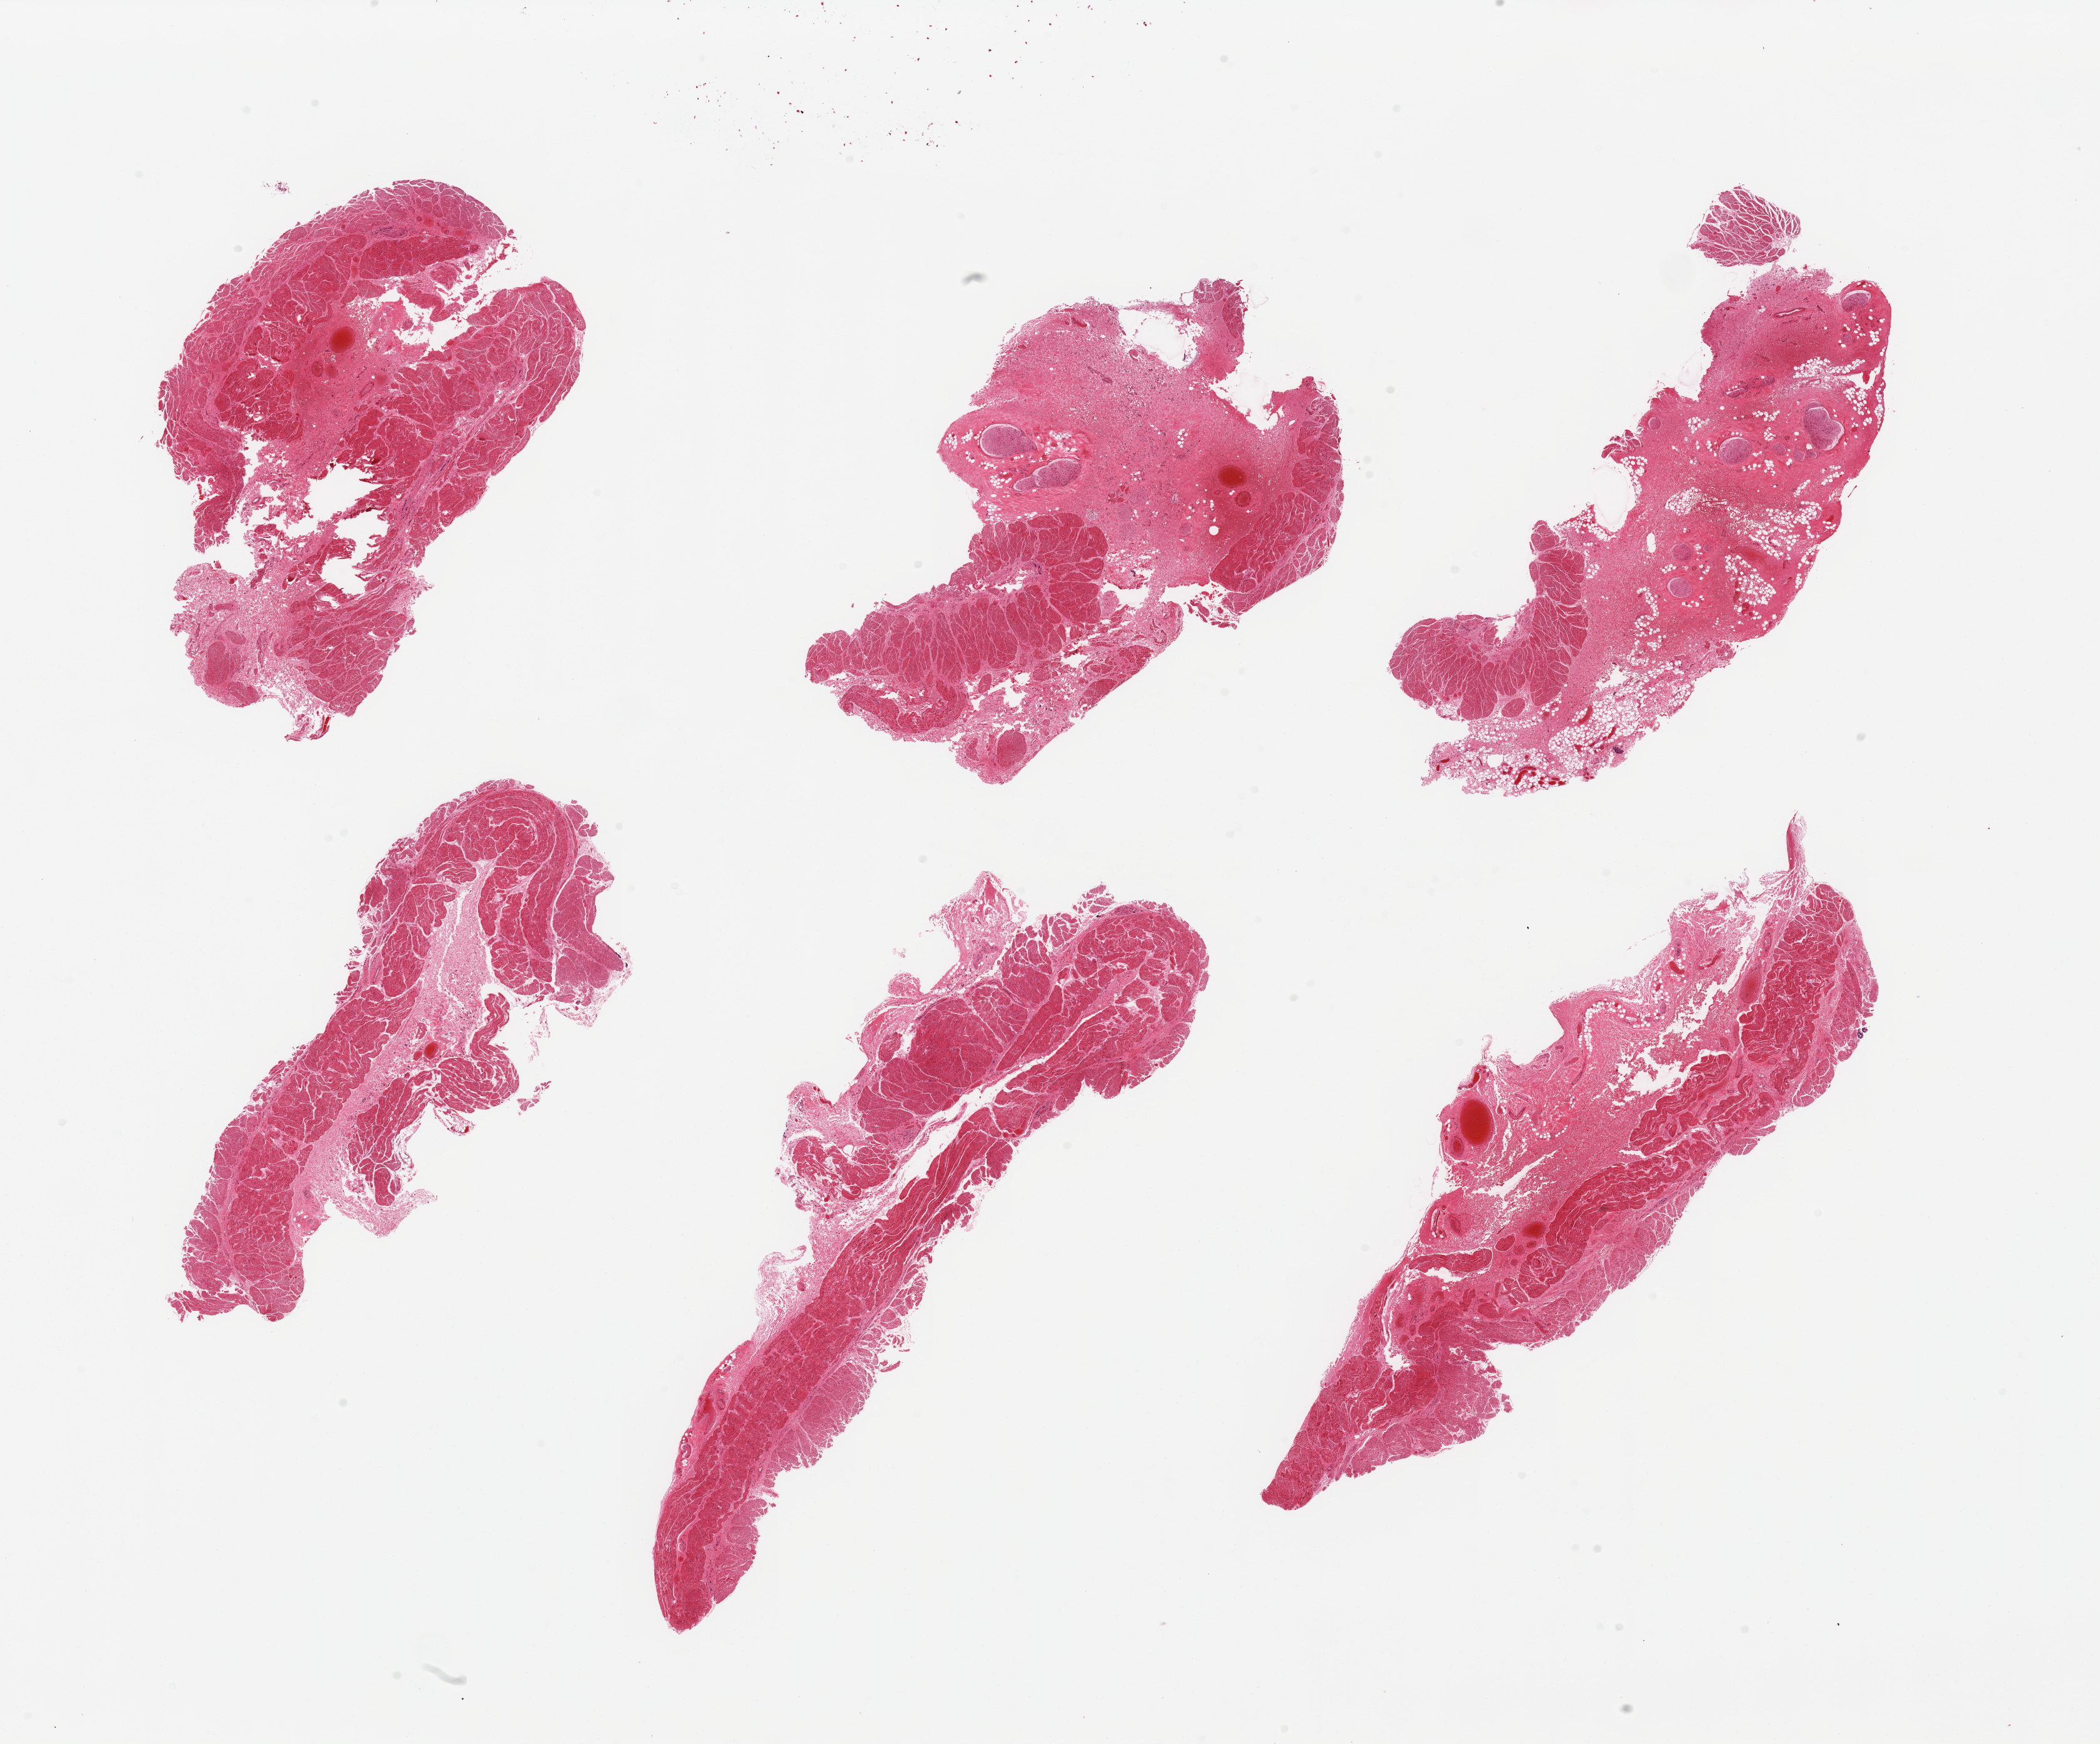
Whole-slide image, hematoxylin and eosin (H&E) stain — whole scanned area (about 26.6 x 22.1 mm) shown as a low-resolution overview. PAXgene-fixed paraffin-embedded (PFPE) section. Section of esophageal muscle (target tissue). Donor tissue sample. Male donor.
- reviewer comment on this tissue sample: 6 pieces; up to 40% fibrous and fatty content